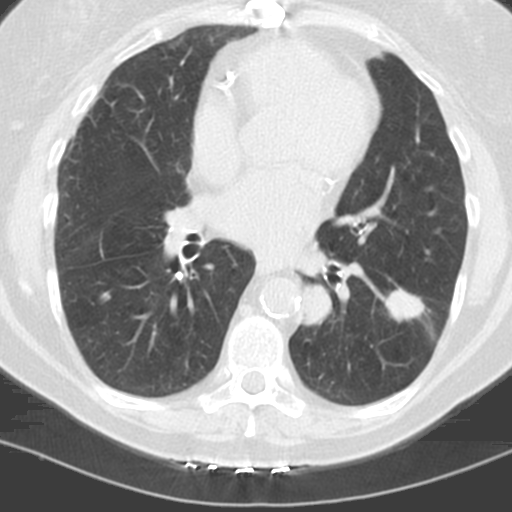
Low-dose screening chest CT, one axial slice. Slice 53 of 121 in the series (ordered by position). Lung window (W 1500 / L -600 HU). 3.2 mm slice thickness. 512 × 512 image matrix.
Annotated regions visible in this slice (outlined manually by an expert reader):
- lesion 1 (tumor, lower lobe of left lung): bounding box (x1, y1, x2, y2) in pixels: (386, 289, 424, 321)
- lesion 2 (tumor, lower lobe of left lung): (303, 285, 332, 324)